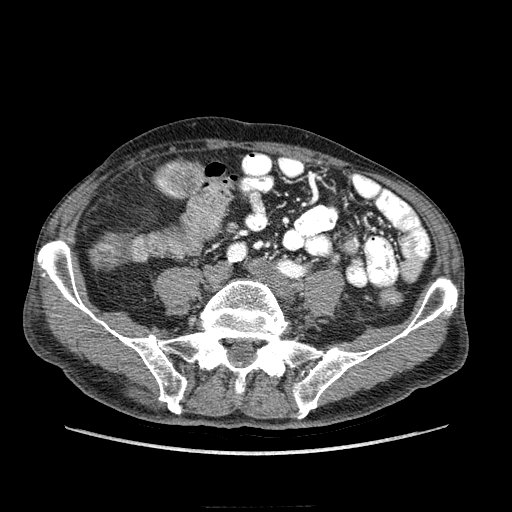
Contrast-enhanced abdominal CT (liver protocol), one axial slice. Slice 23 of 218 in the series (ordered by position). 100 kVp. Soft-tissue window (W 400 / L 40 HU). 2.5 mm slice thickness. 512 × 512 image matrix, field of view 380 × 380 mm. From the clinical record (not read from this slice): diagnosis: hepatocellular carcinoma (patient treated with transarterial chemoembolisation; whether this scan precedes or follows treatment is not stated here); TNM stage (as recorded): Stage-IIIA.
Outlined on this slice (semi-automatic segmentation, software-assisted and operator-edited):
- mass: bounding box (x1, y1, x2, y2) in pixels: (167, 163, 201, 196)